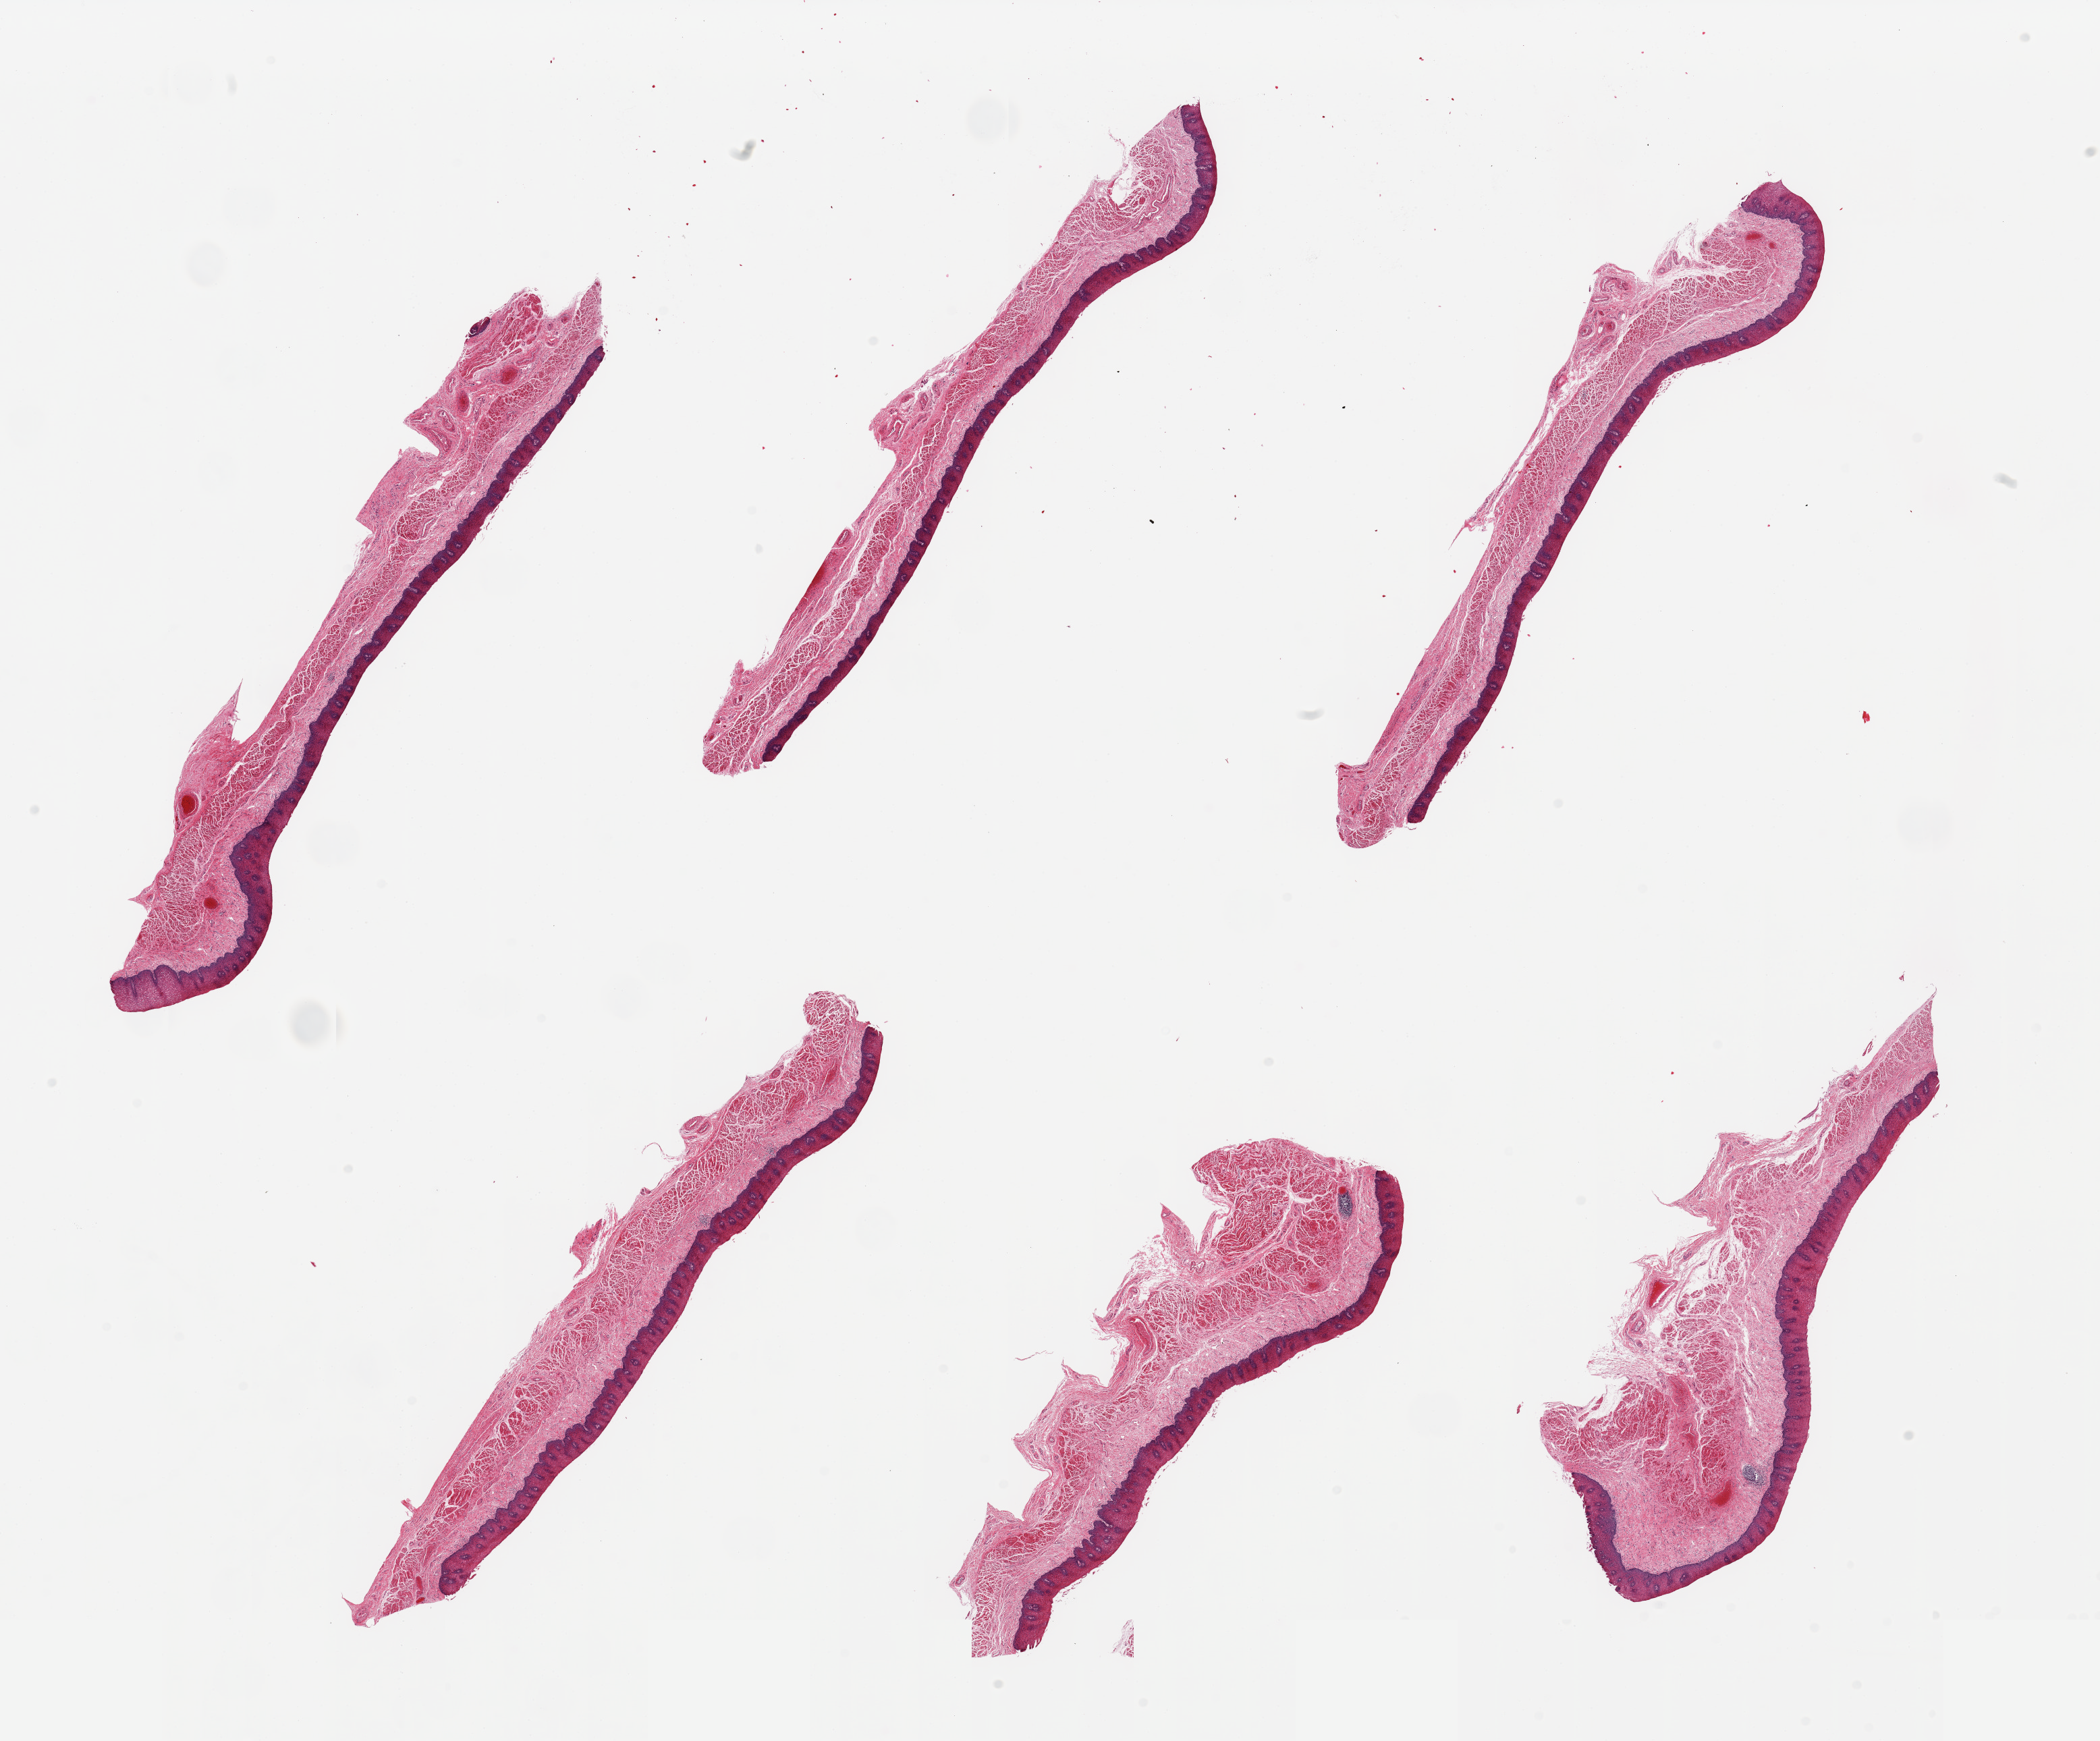
Whole-slide image, haematoxylin and eosin stain, brightfield, whole scanned area (about 24.6 x 20.4 mm) shown as a low-resolution overview, PAXgene-fixed, paraffin-embedded tissue, section of esophageal mucous membrane (target tissue), donor tissue sample. Donor: male.
• review note (as recorded): 6 pieces